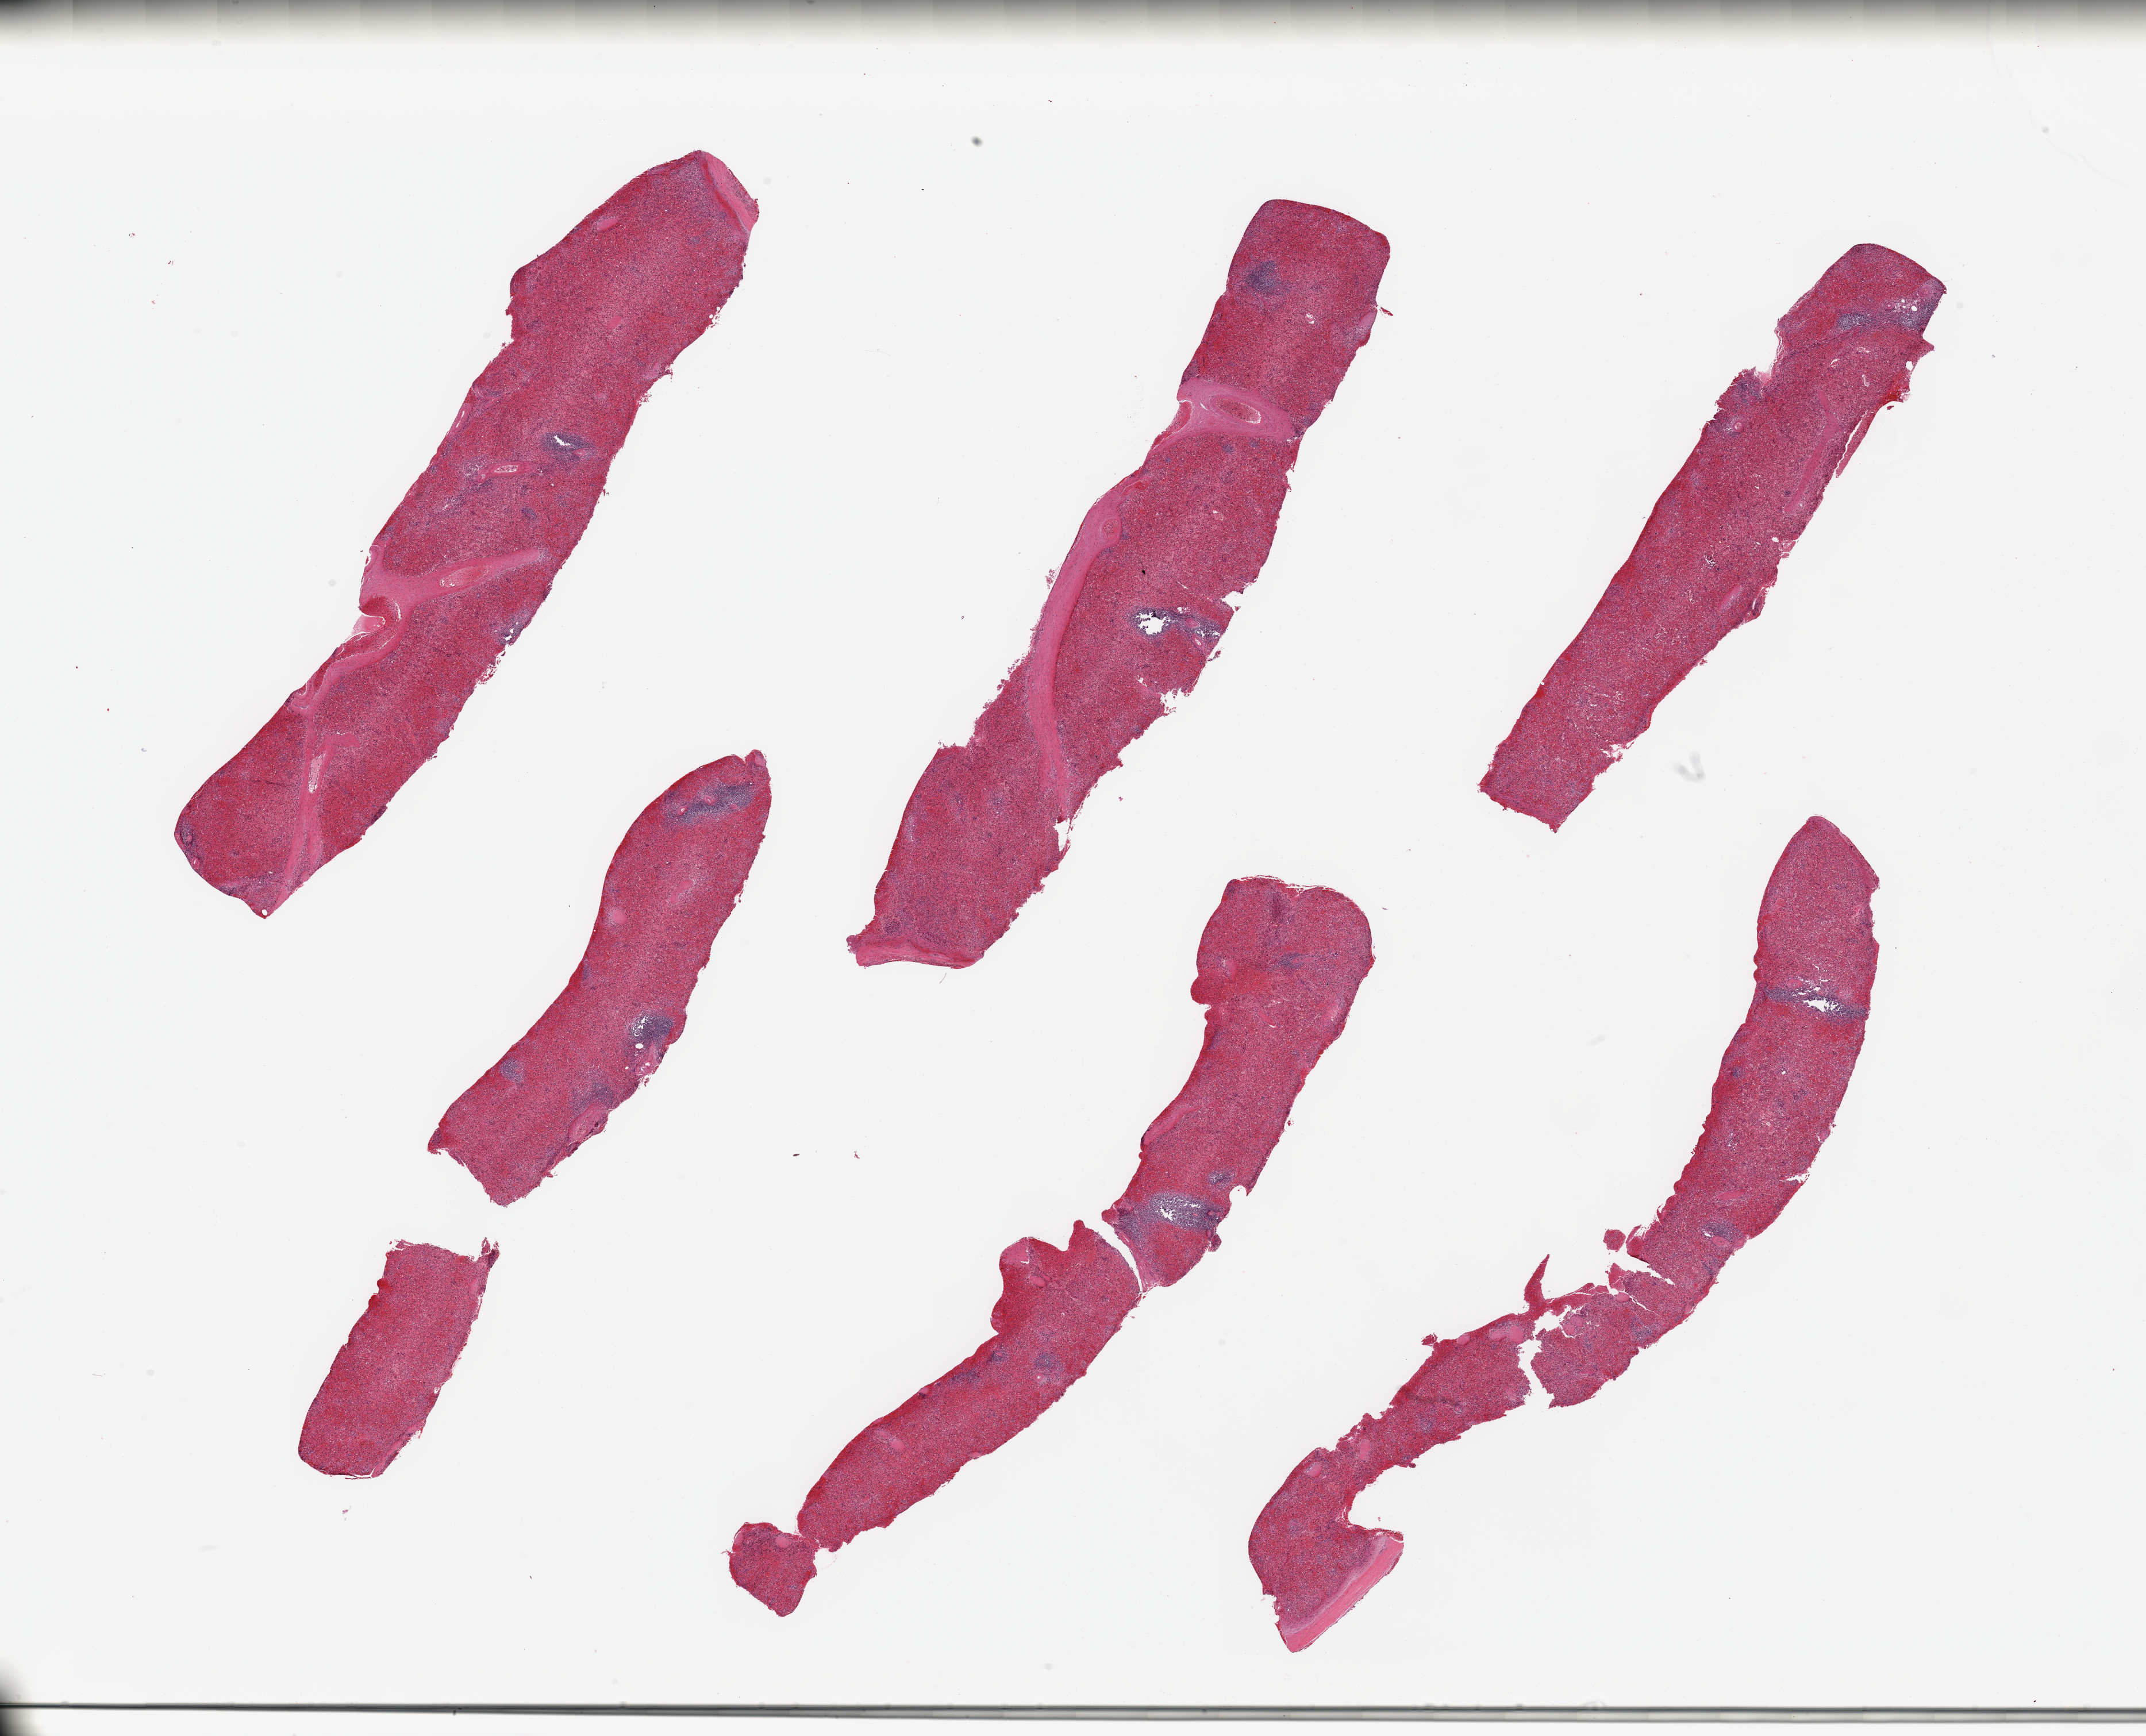
Digitized H&E-stained section — low-resolution overview of the scanned area, about 29.5 x 23.9 mm; PAXgene-fixed, paraffin-embedded tissue; target tissue: spleen; donor tissue sample. Donor: male.
Pathologist's review note for this sample: 6 pieces; congested spleen.